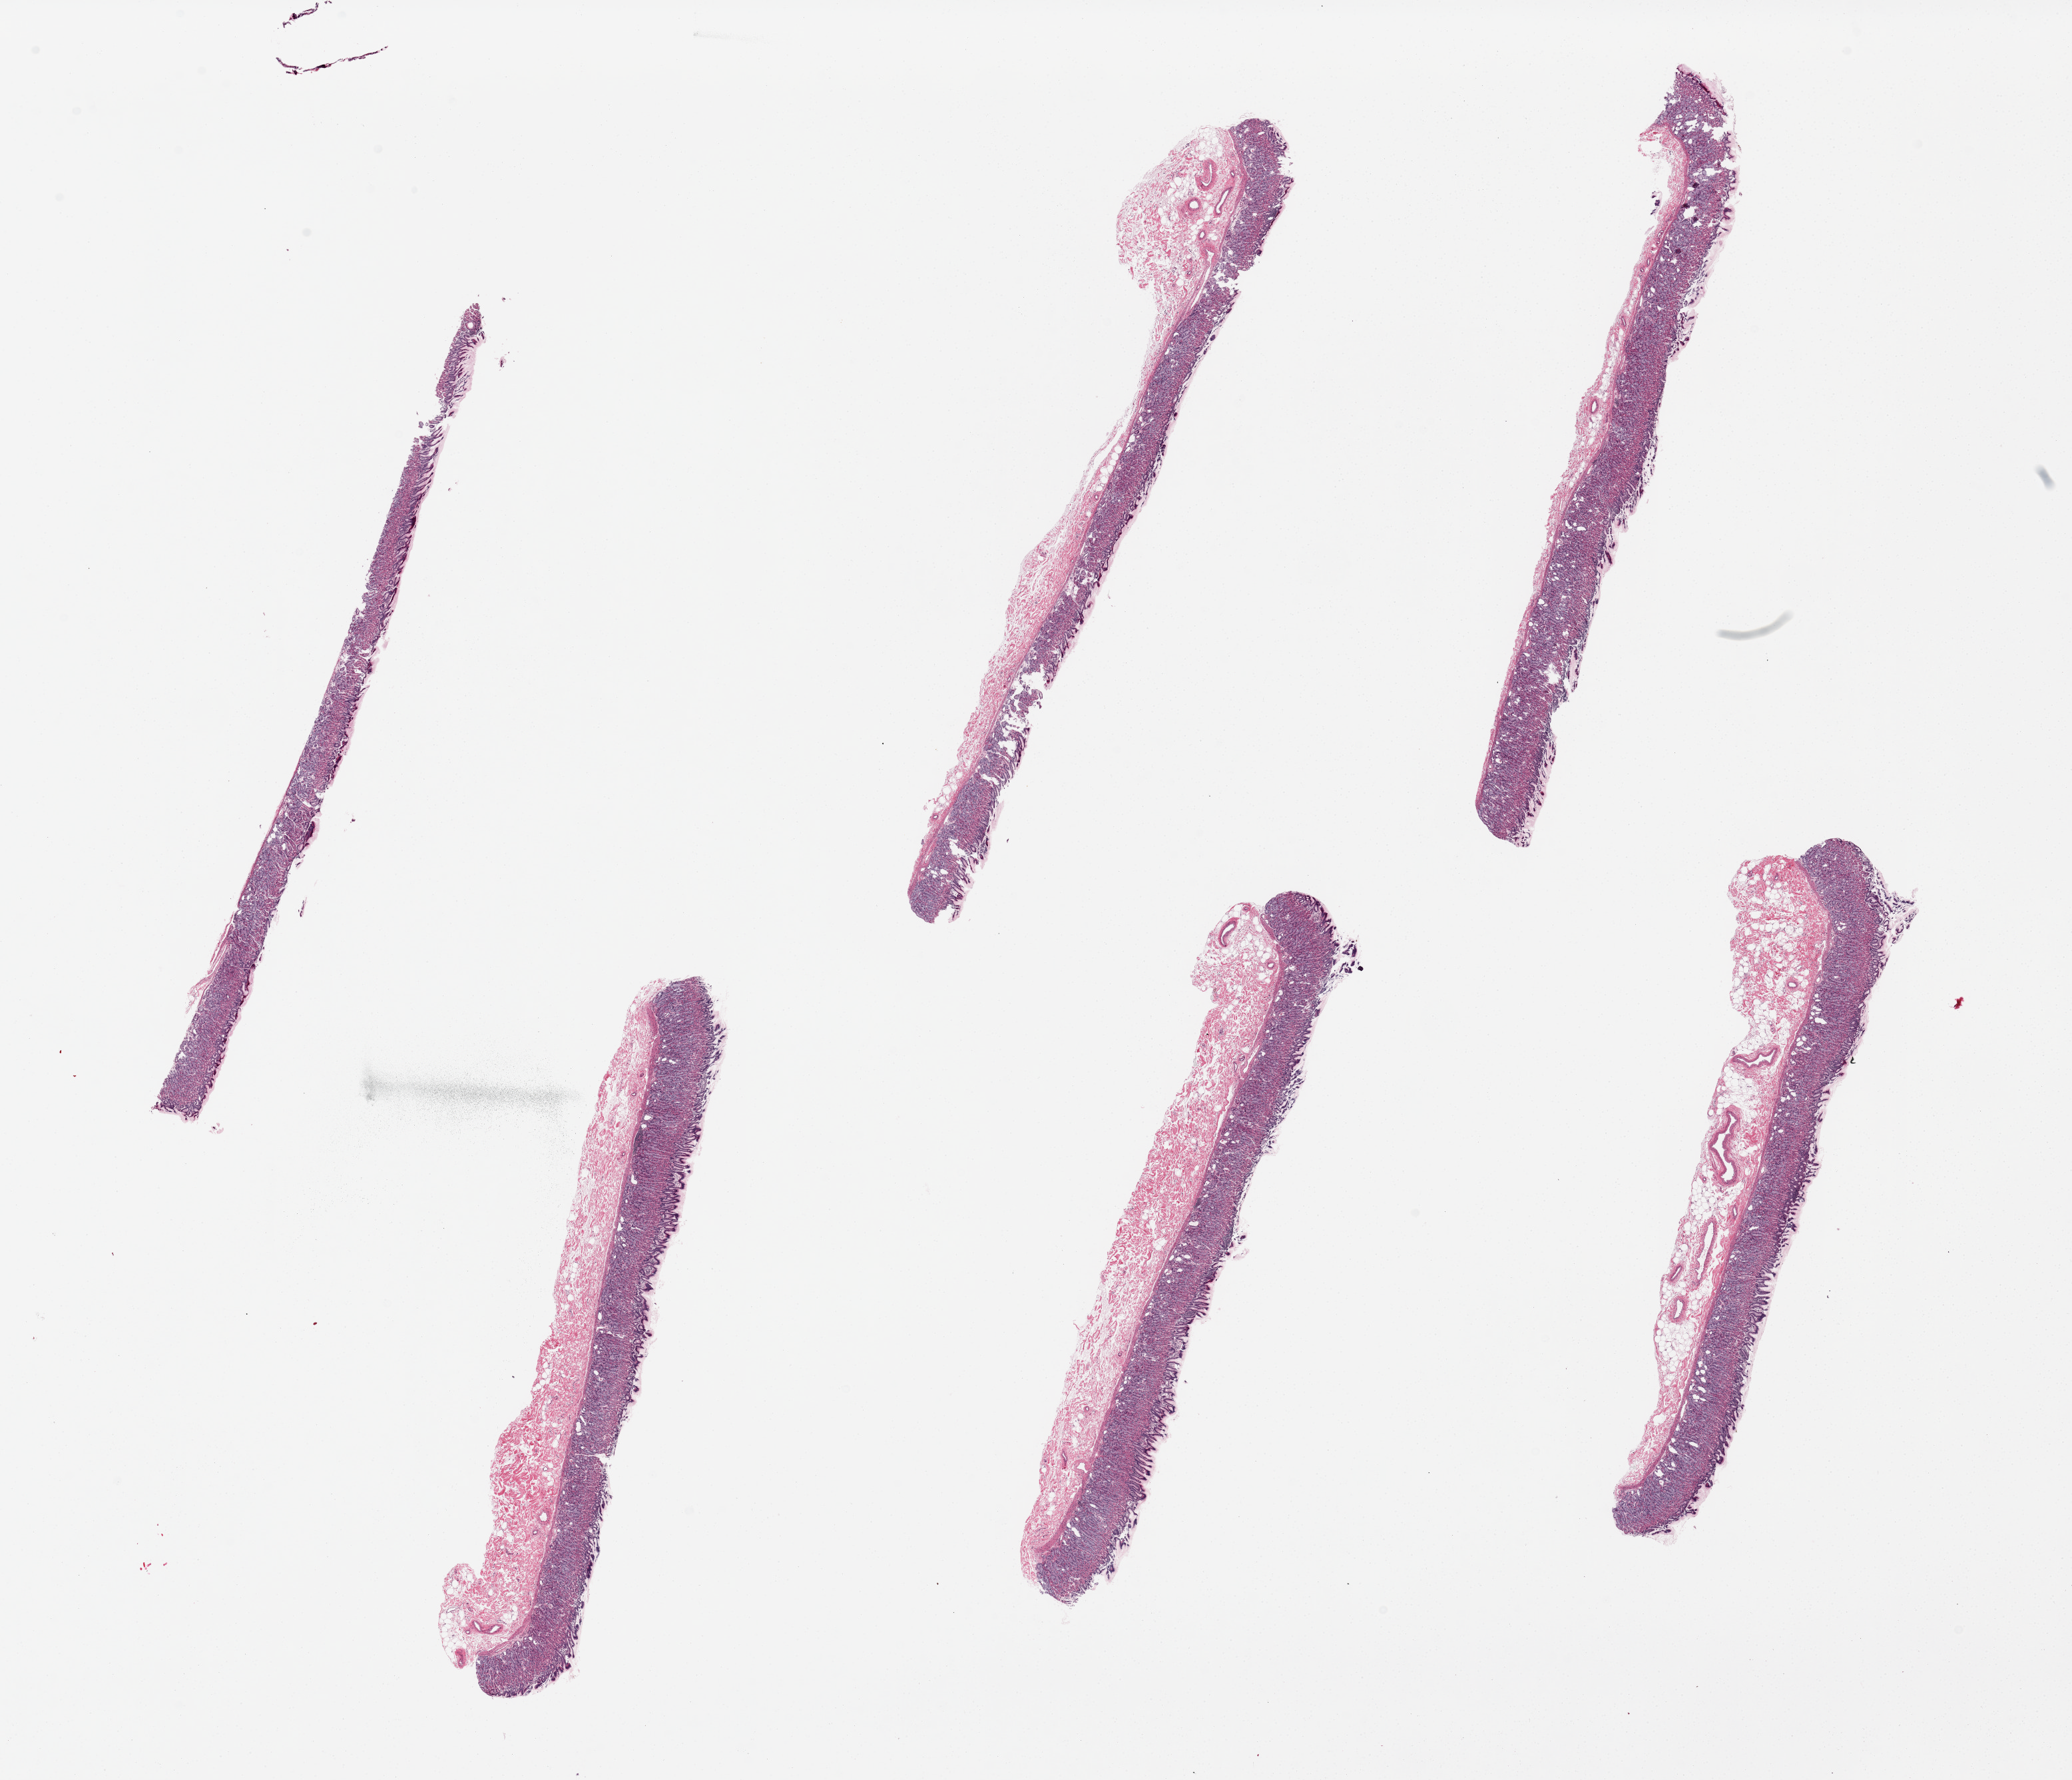
Hematoxylin and eosin (H&E) whole-slide image — shown as a low-resolution overview of the whole scanned area (about 24.6 x 21.1 mm). PAXgene-fixed, paraffin-embedded tissue. Sampled site (target tissue): stomach. Donor tissue sample. Male donor.
Pathologist's review note for this sample: 6 pieces; mucosa and submucosa.